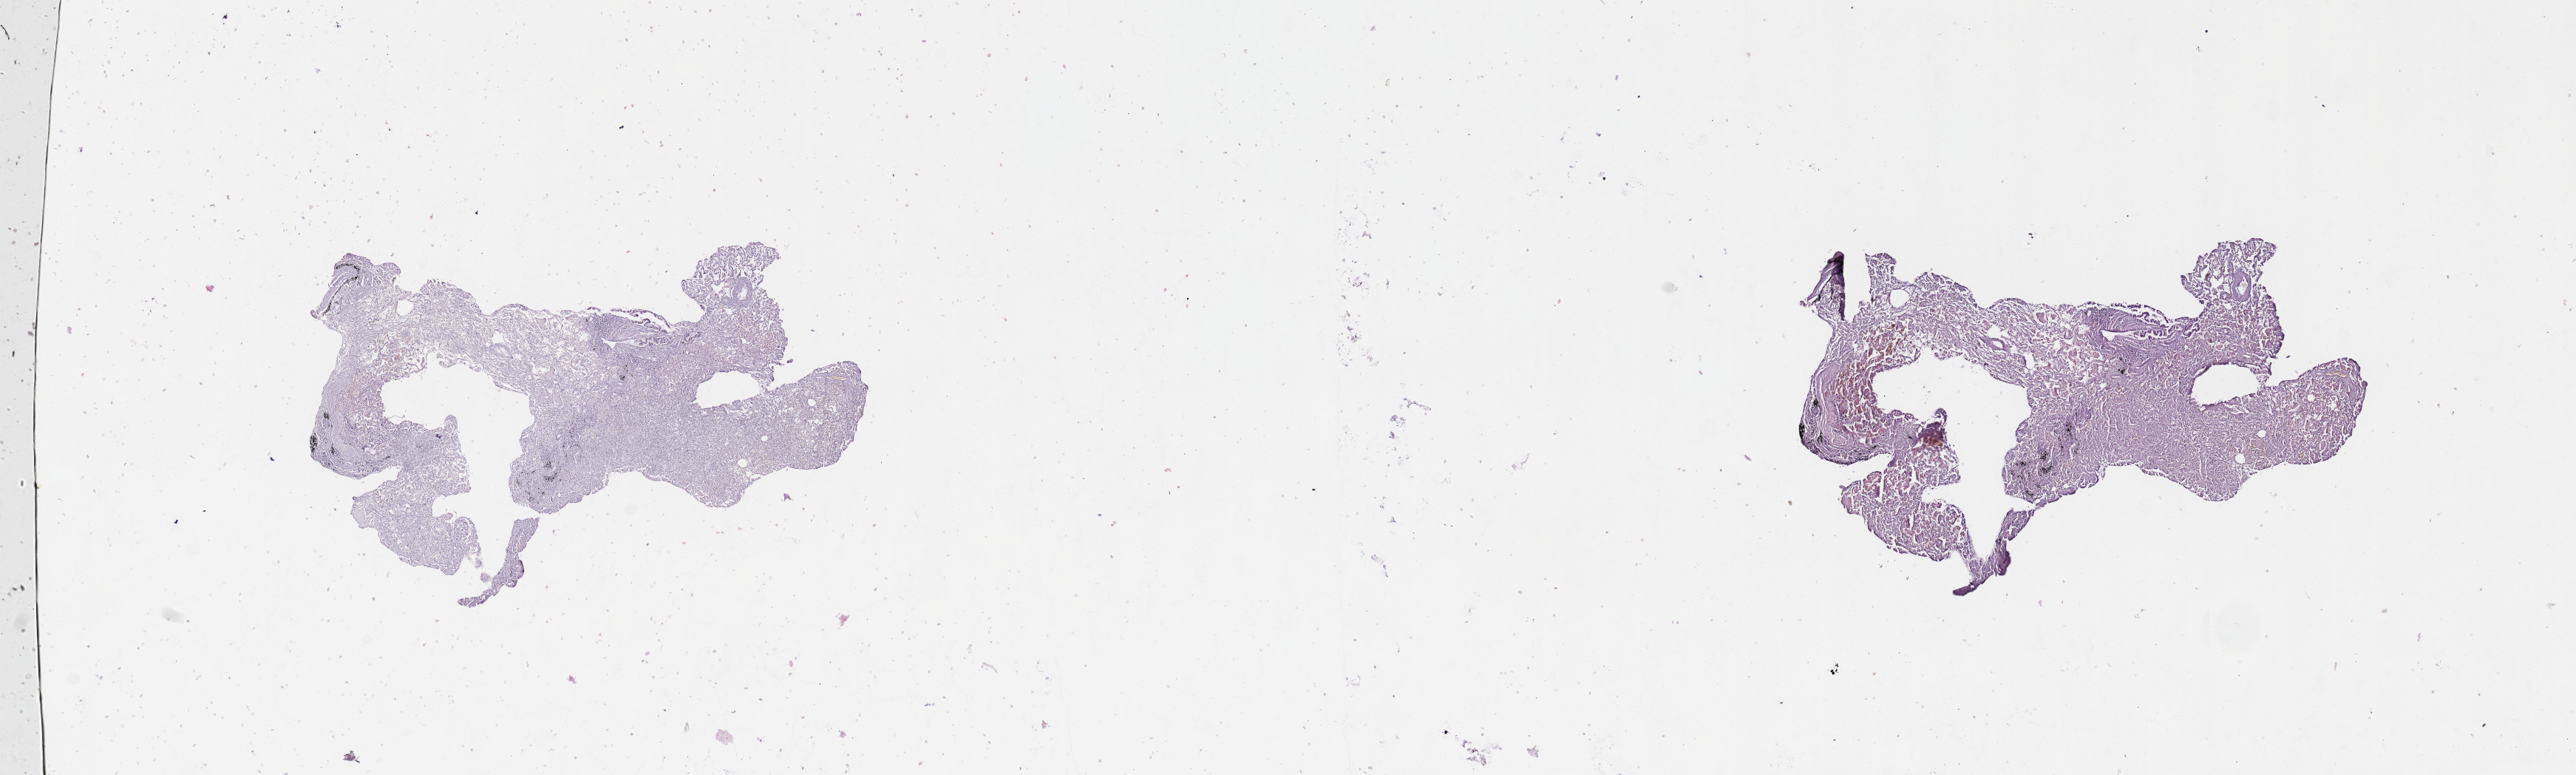
Whole-slide histology image, Hematoxylin and eosin (H&E) stained — shown as a low-resolution overview of the whole scanned area (about 27.6 x 8.3 mm, from a 20x scan), normal (non-tumour) tissue sample, lung. 74-year-old male patient.
This section: normal (non-tumour) tissue from the same patient. Patient diagnosis: Squamous cell carcinoma, NOS.